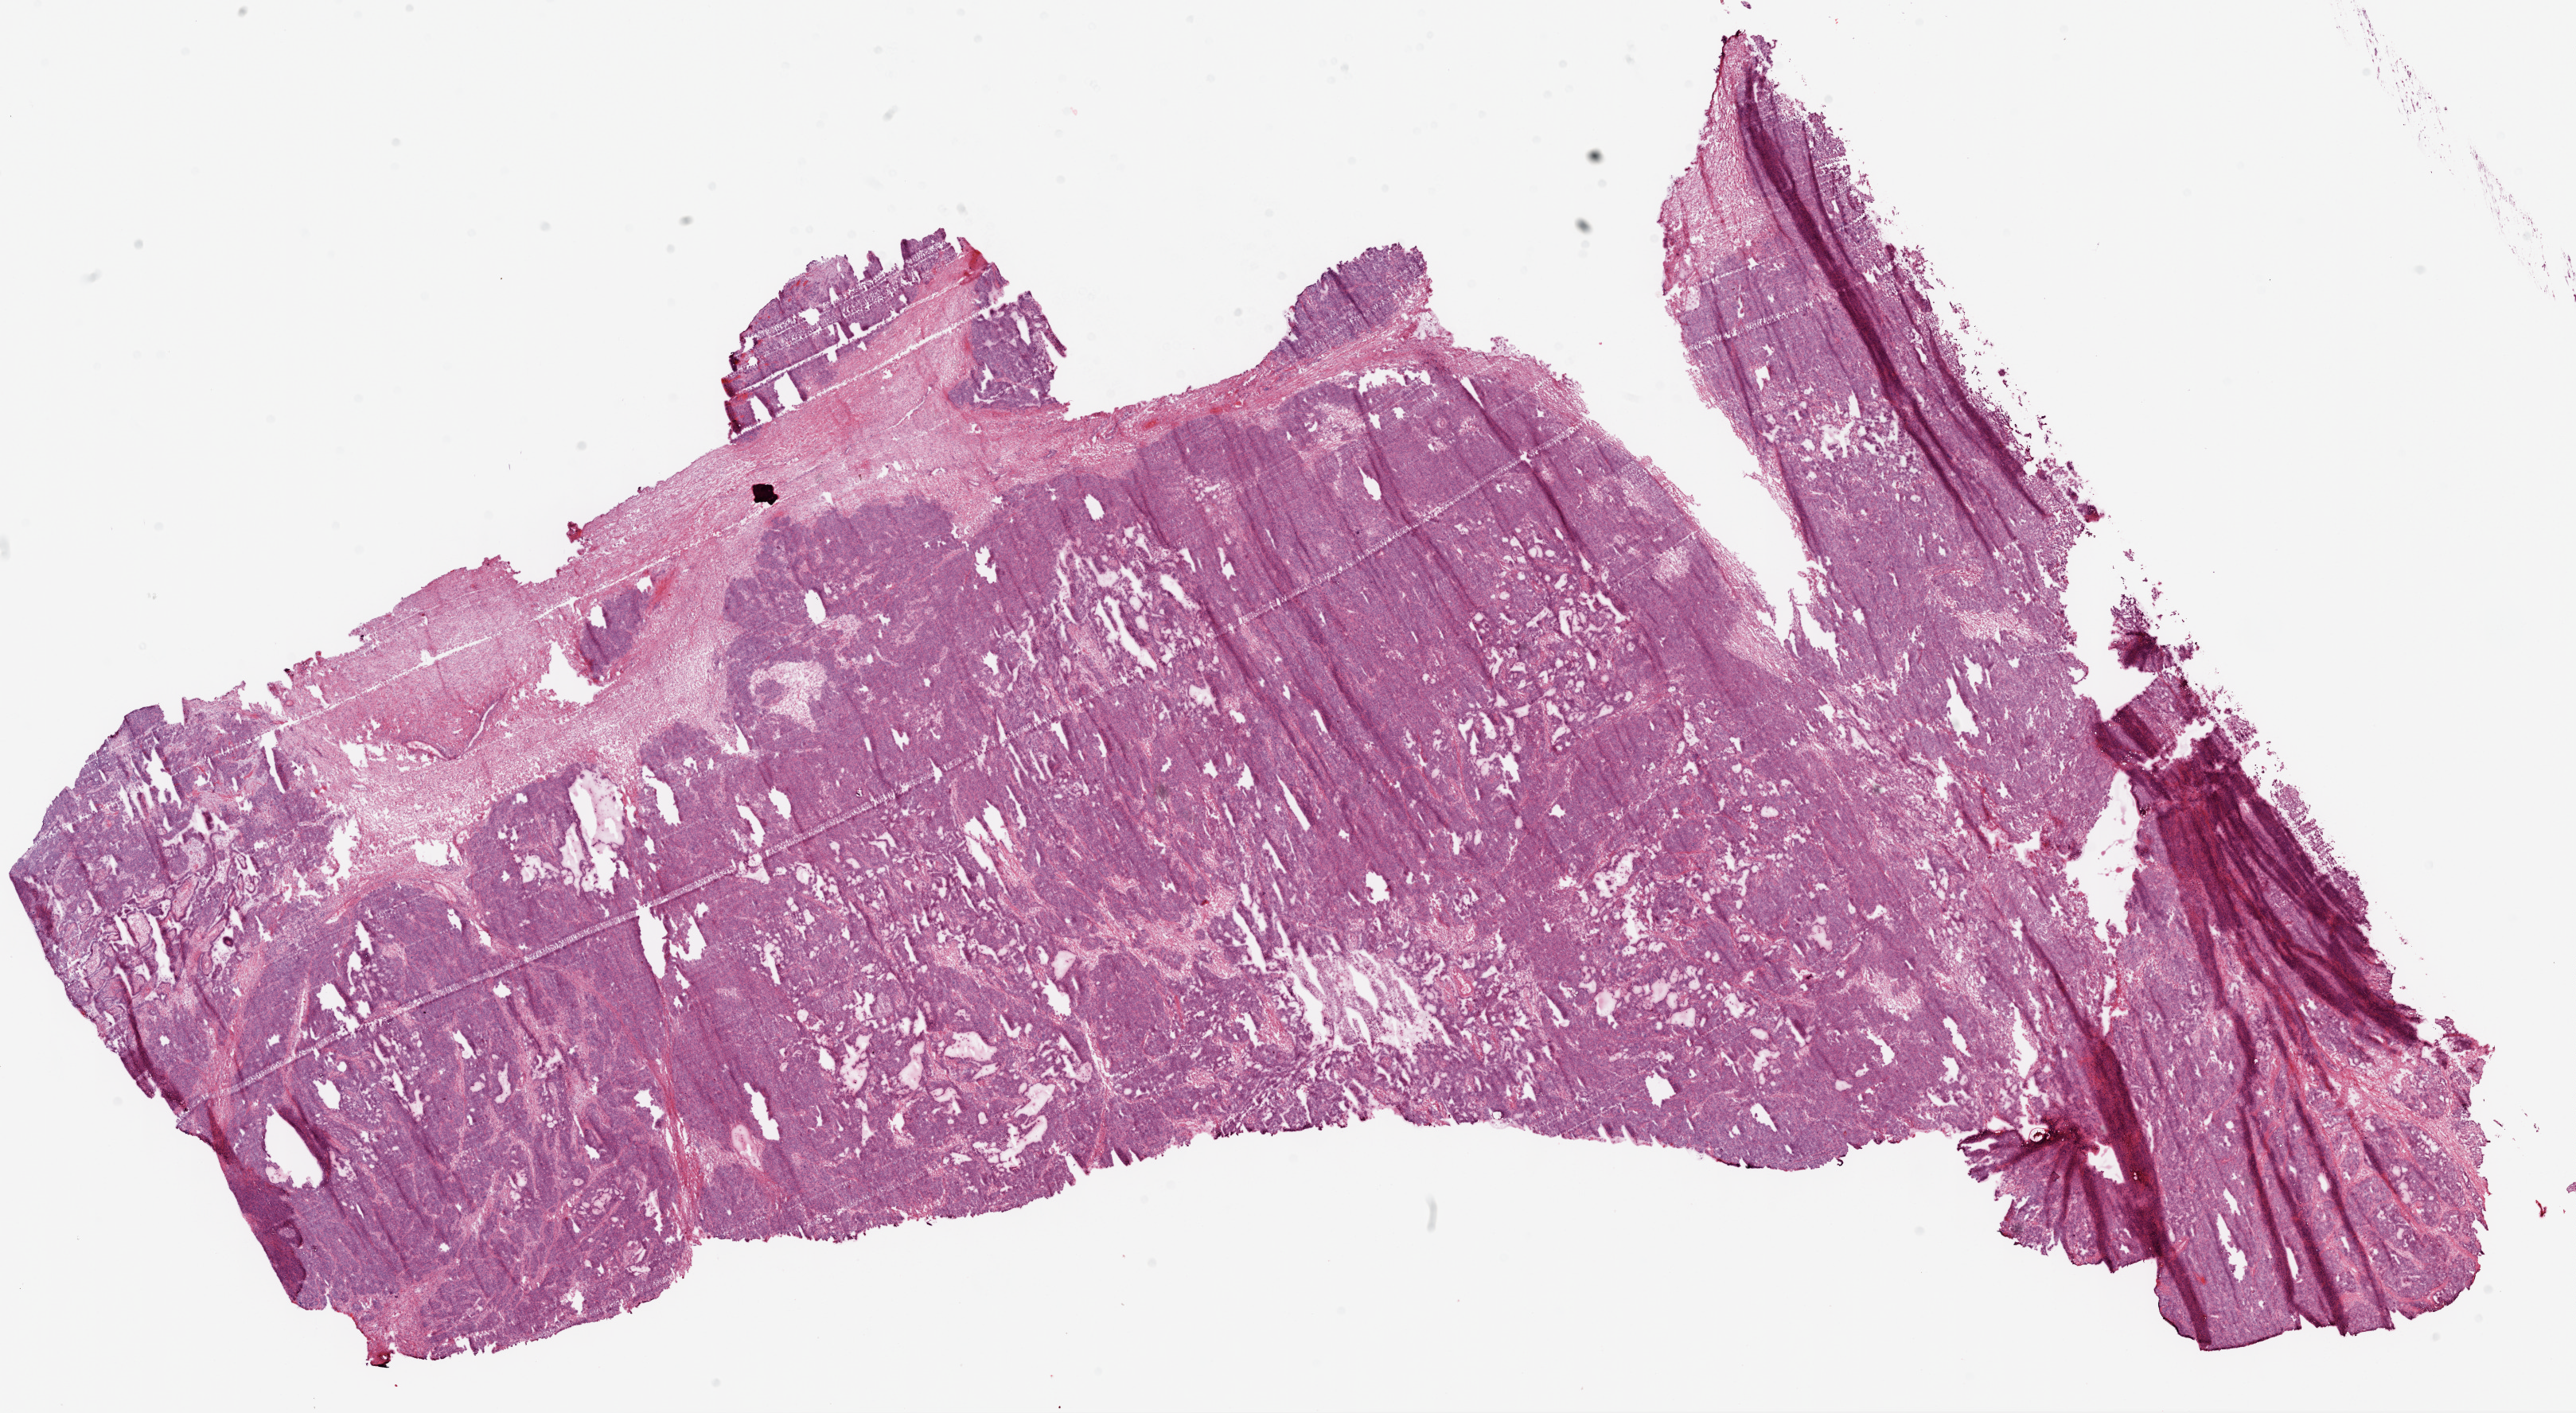
Whole-slide histology image, Hematoxylin and eosin (H&E) stained, a low-resolution overview of the entire scanned area, about 26.1 x 14.3 mm (slide scanned at 20x); frozen section; sample: primary tumour, ovary. Female patient; age at initial diagnosis 69 years. Histologic grade: G3 (poorly differentiated). Pathologist review of this section (percent, as recorded): tumour cells 90%, tumour nuclei 95%, normal cells 0%, stromal cells 10%, necrosis 0%.
• FIGO stage: IV
• pathologic diagnosis: Serous cystadenocarcinoma, NOS